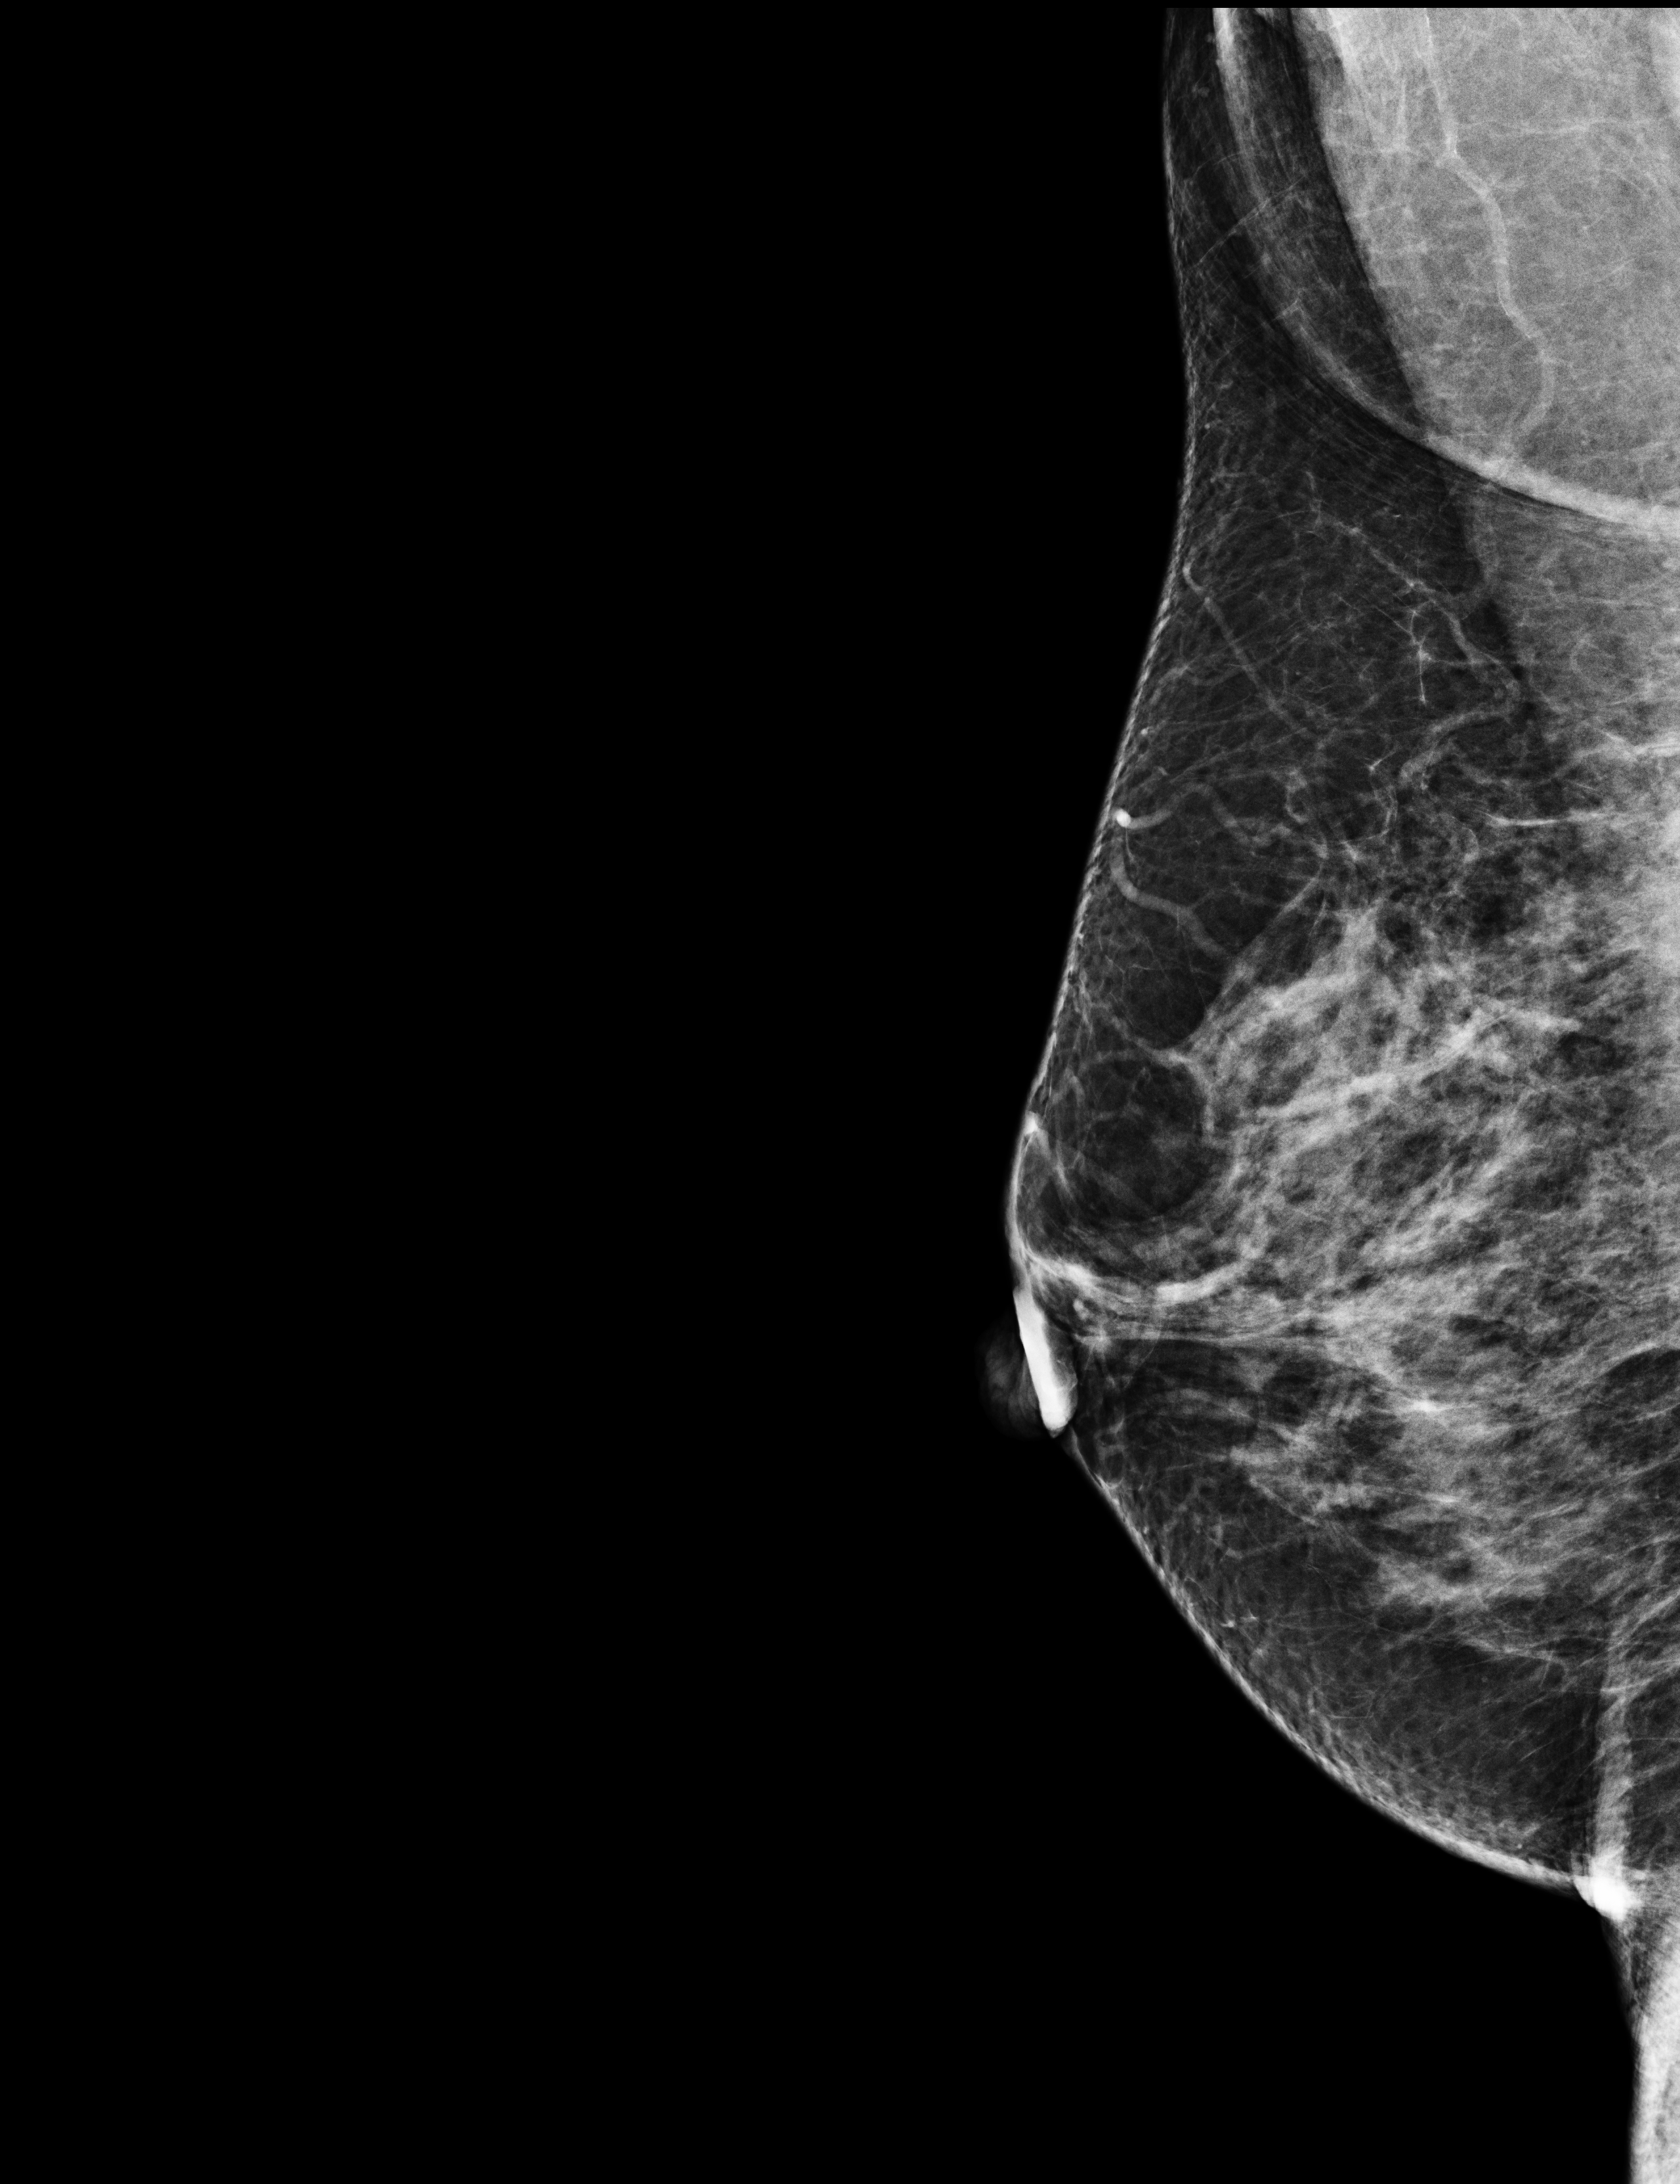
Screening examination. Patient aged 62 years (female).
Image type: full-field digital mammogram. Breast: right. Projection: MLO view.